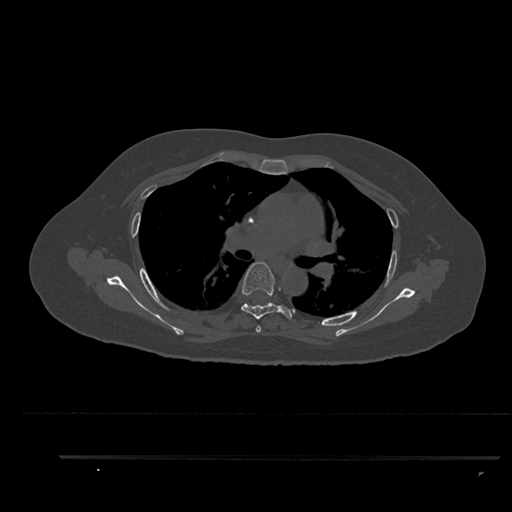
CT including the spine, one axial slice; position 602 of 797 along the scan axis; reconstruction kernel Br40s/3; bone window (W 1800 / L 400 HU); 512 × 512 image matrix, field of view 408 × 408 mm. Patient: female, 44 years. Case-level facts recorded for this patient, not image findings: primary cancer: renal.
Structures marked on this image (semi-automatically segmented with operator editing):
- T4 vertebra: bounding box [x1, y1, x2, y2] px = [256, 325, 261, 333]
- T5 vertebra: [241, 262, 292, 320]
- T6 vertebra: [264, 304, 268, 306]